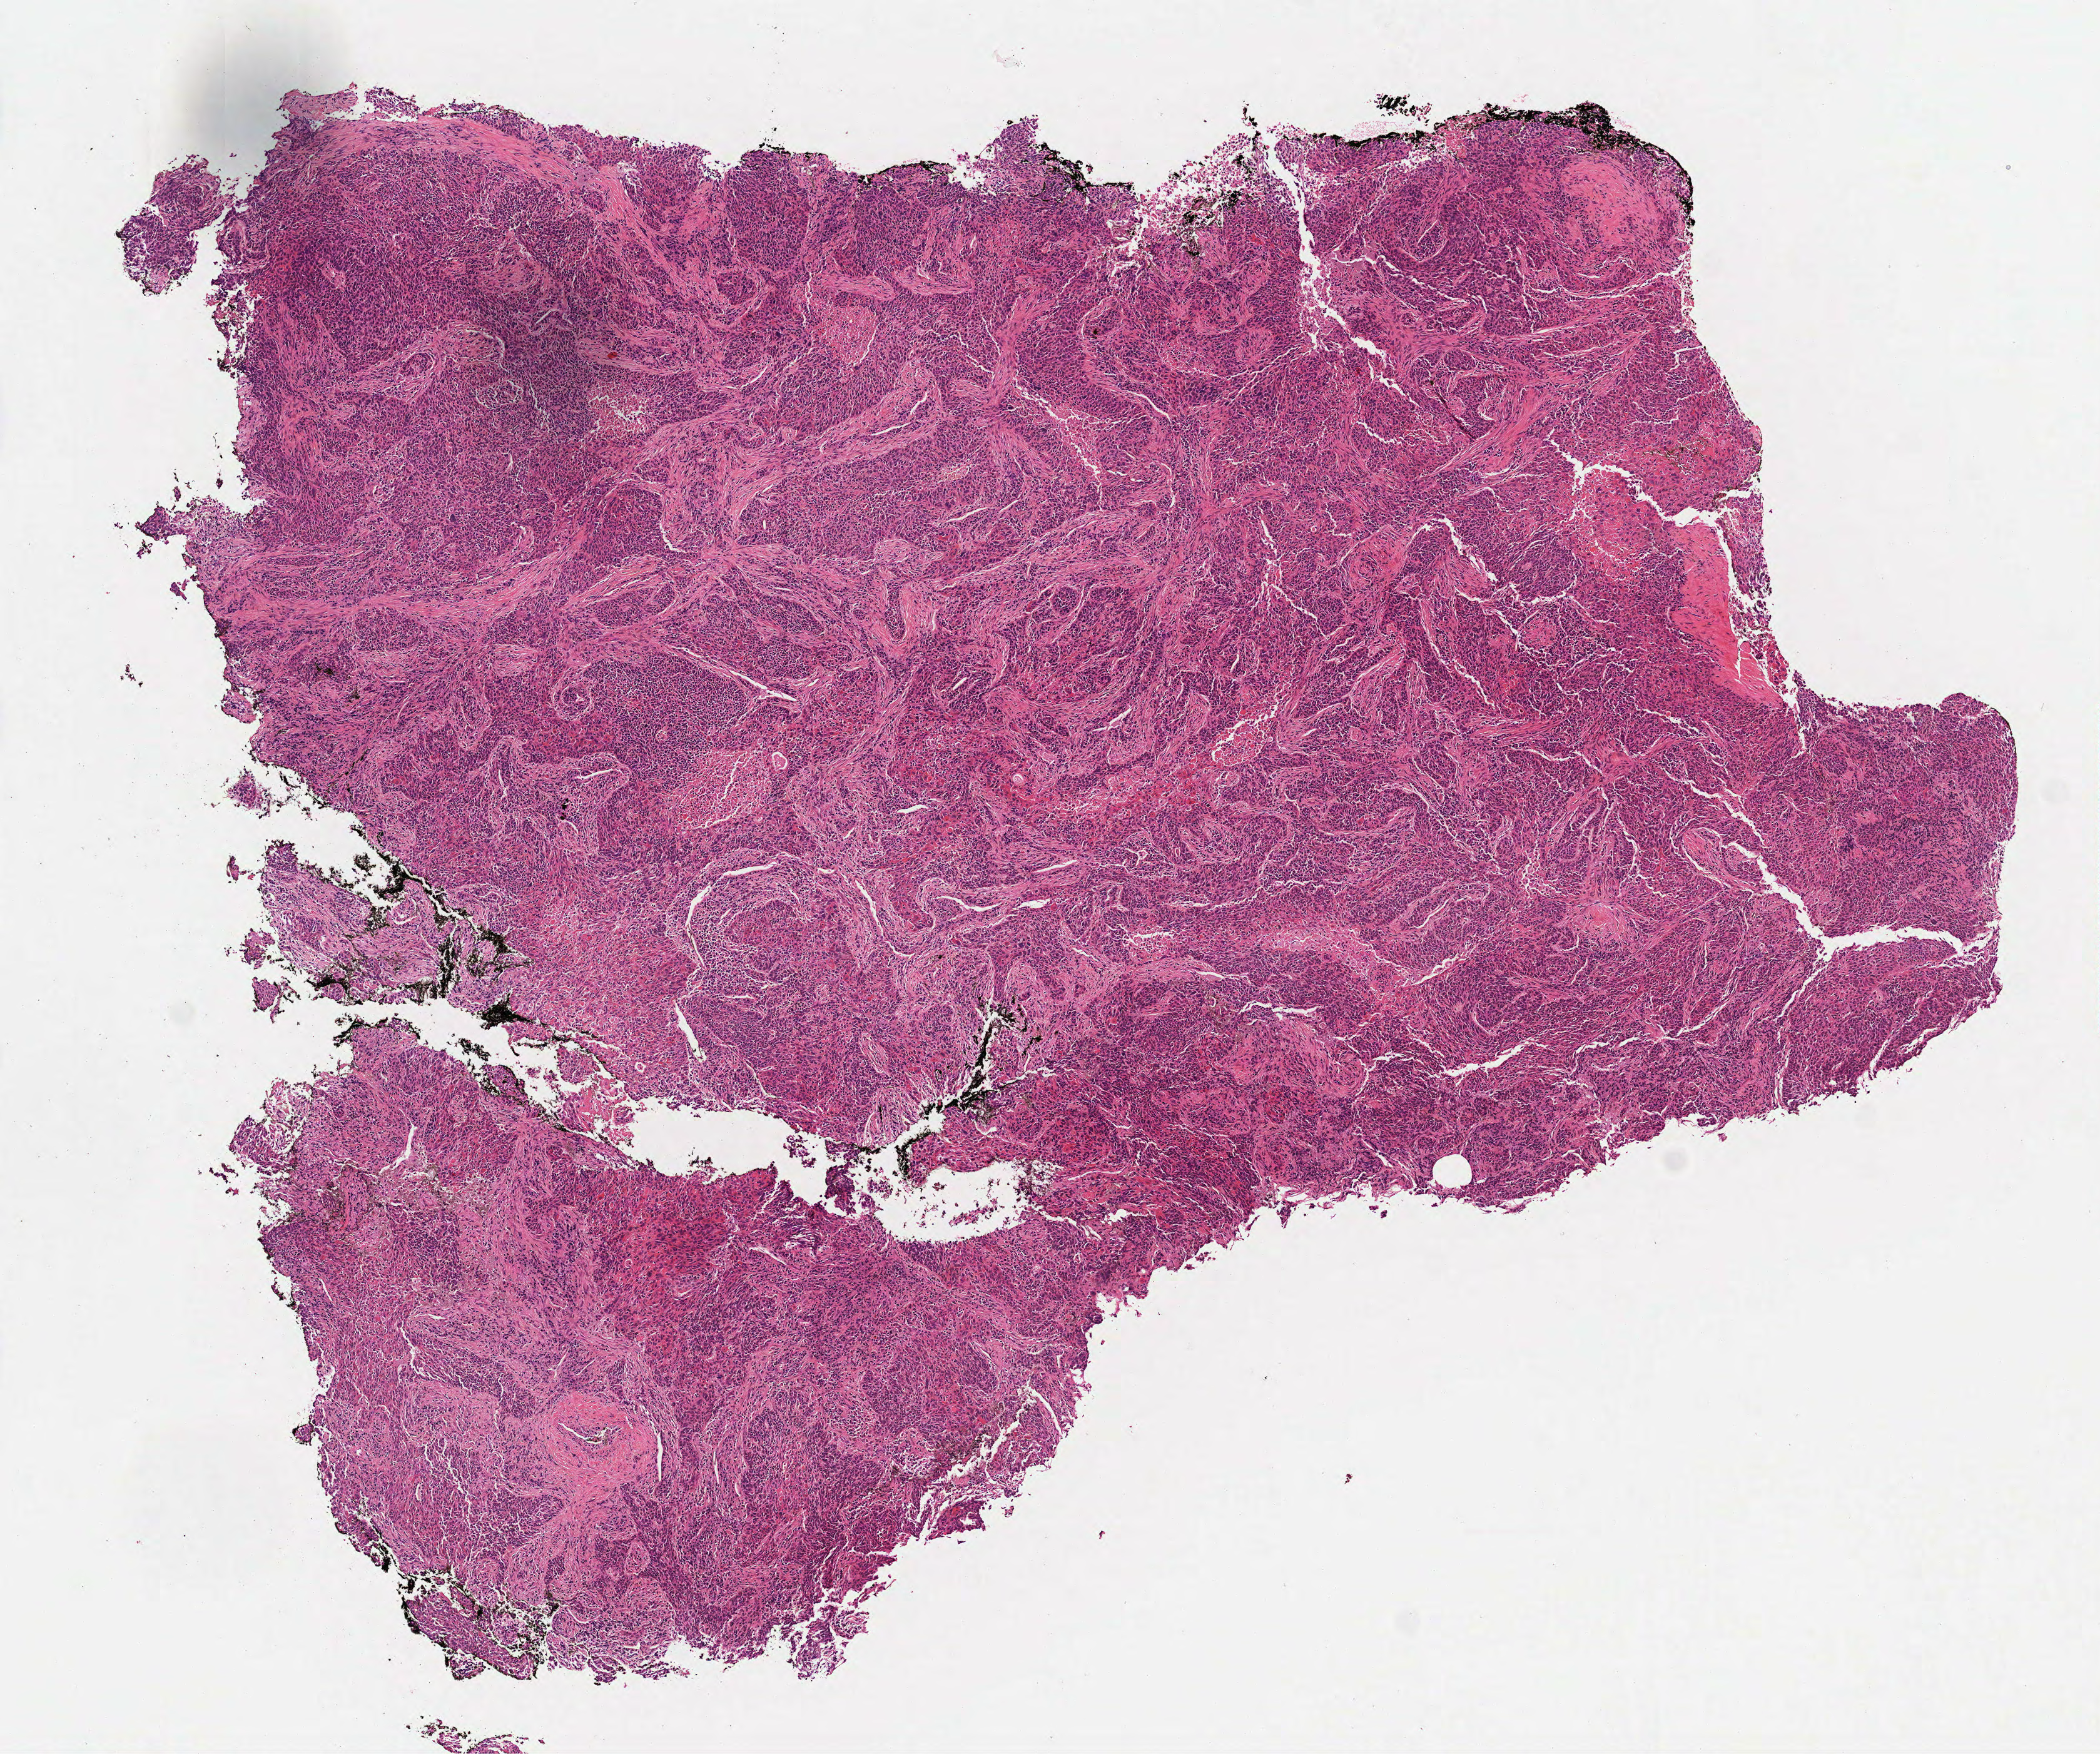
Digitized H&E tissue section (whole slide), low-resolution overview of the scanned area, about 6.8 x 5.7 mm (slide scanned at 40x); frozen section from the top of the tissue portion; primary tumour sample from the lung. Male patient; age at initial diagnosis 58 years. Slide review estimates, as recorded: tumour cells 100%, tumour nuclei 70%, normal cells 0%, stromal cells 0%, necrosis 0%. Infiltration values recorded for this section: lymphocyte infiltration 15%, monocyte infiltration 0%, neutrophil infiltration 2%.
* laterality: right
* AJCC pathologic stage: IIA (7th edition)
* pathologic diagnosis: Squamous cell carcinoma, NOS (upper lobe, lung)